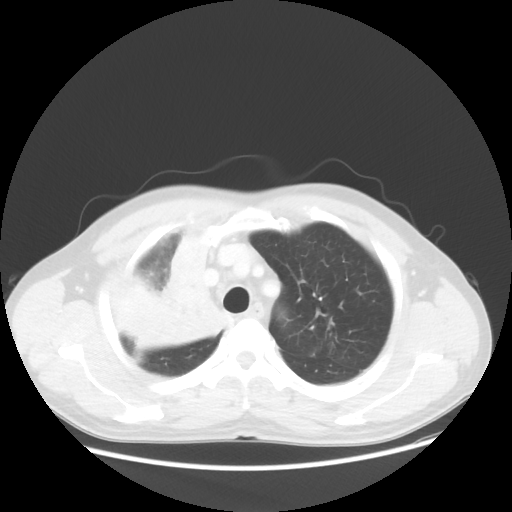
Chest CT, one axial slice; slice 43 of 56 in the series (ordered by position); 100 kVp; lung window (W 1500 / L -600 HU); 5 mm slice thickness; 512 × 512 image matrix, field of view 398 × 398 mm. Patient: male, 60 years. From the clinical record (not read from this slice): clinical TNM (as recorded): T2a N1 M0.
Structures marked on this image (bounding box drawn by a radiologist):
- lung tumour (recorded histology: squamous cell carcinoma): bounding box (x1, y1, x2, y2) in pixels: (101, 231, 226, 344)